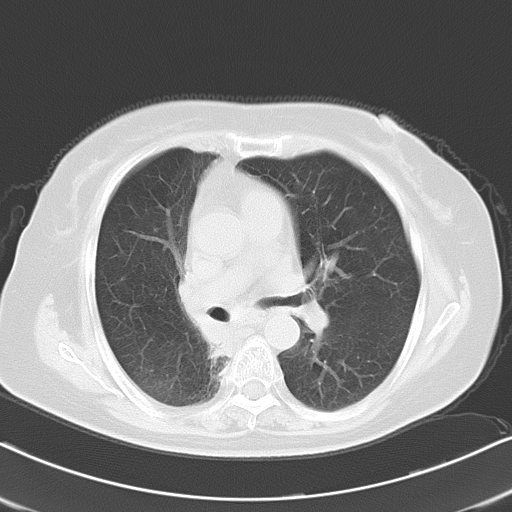
Chest CT, one axial slice. Position 12 of 21 along the scan axis. Reconstruction kernel B70f. 120 kVp. Lung window (W 1500 / L -600 HU). 10 mm slice thickness. 512 × 512 image matrix, field of view 326 × 326 mm. Patient: female, 61 years. Case-level facts recorded for this patient, not image findings: clinical TNM (as recorded): T1b N0 M1b.
Structures marked on this image (rectangle marked by the reading radiologist):
- lung tumour (recorded histology: squamous cell carcinoma): bounding box (x1, y1, x2, y2) in pixels: (170, 271, 247, 420)